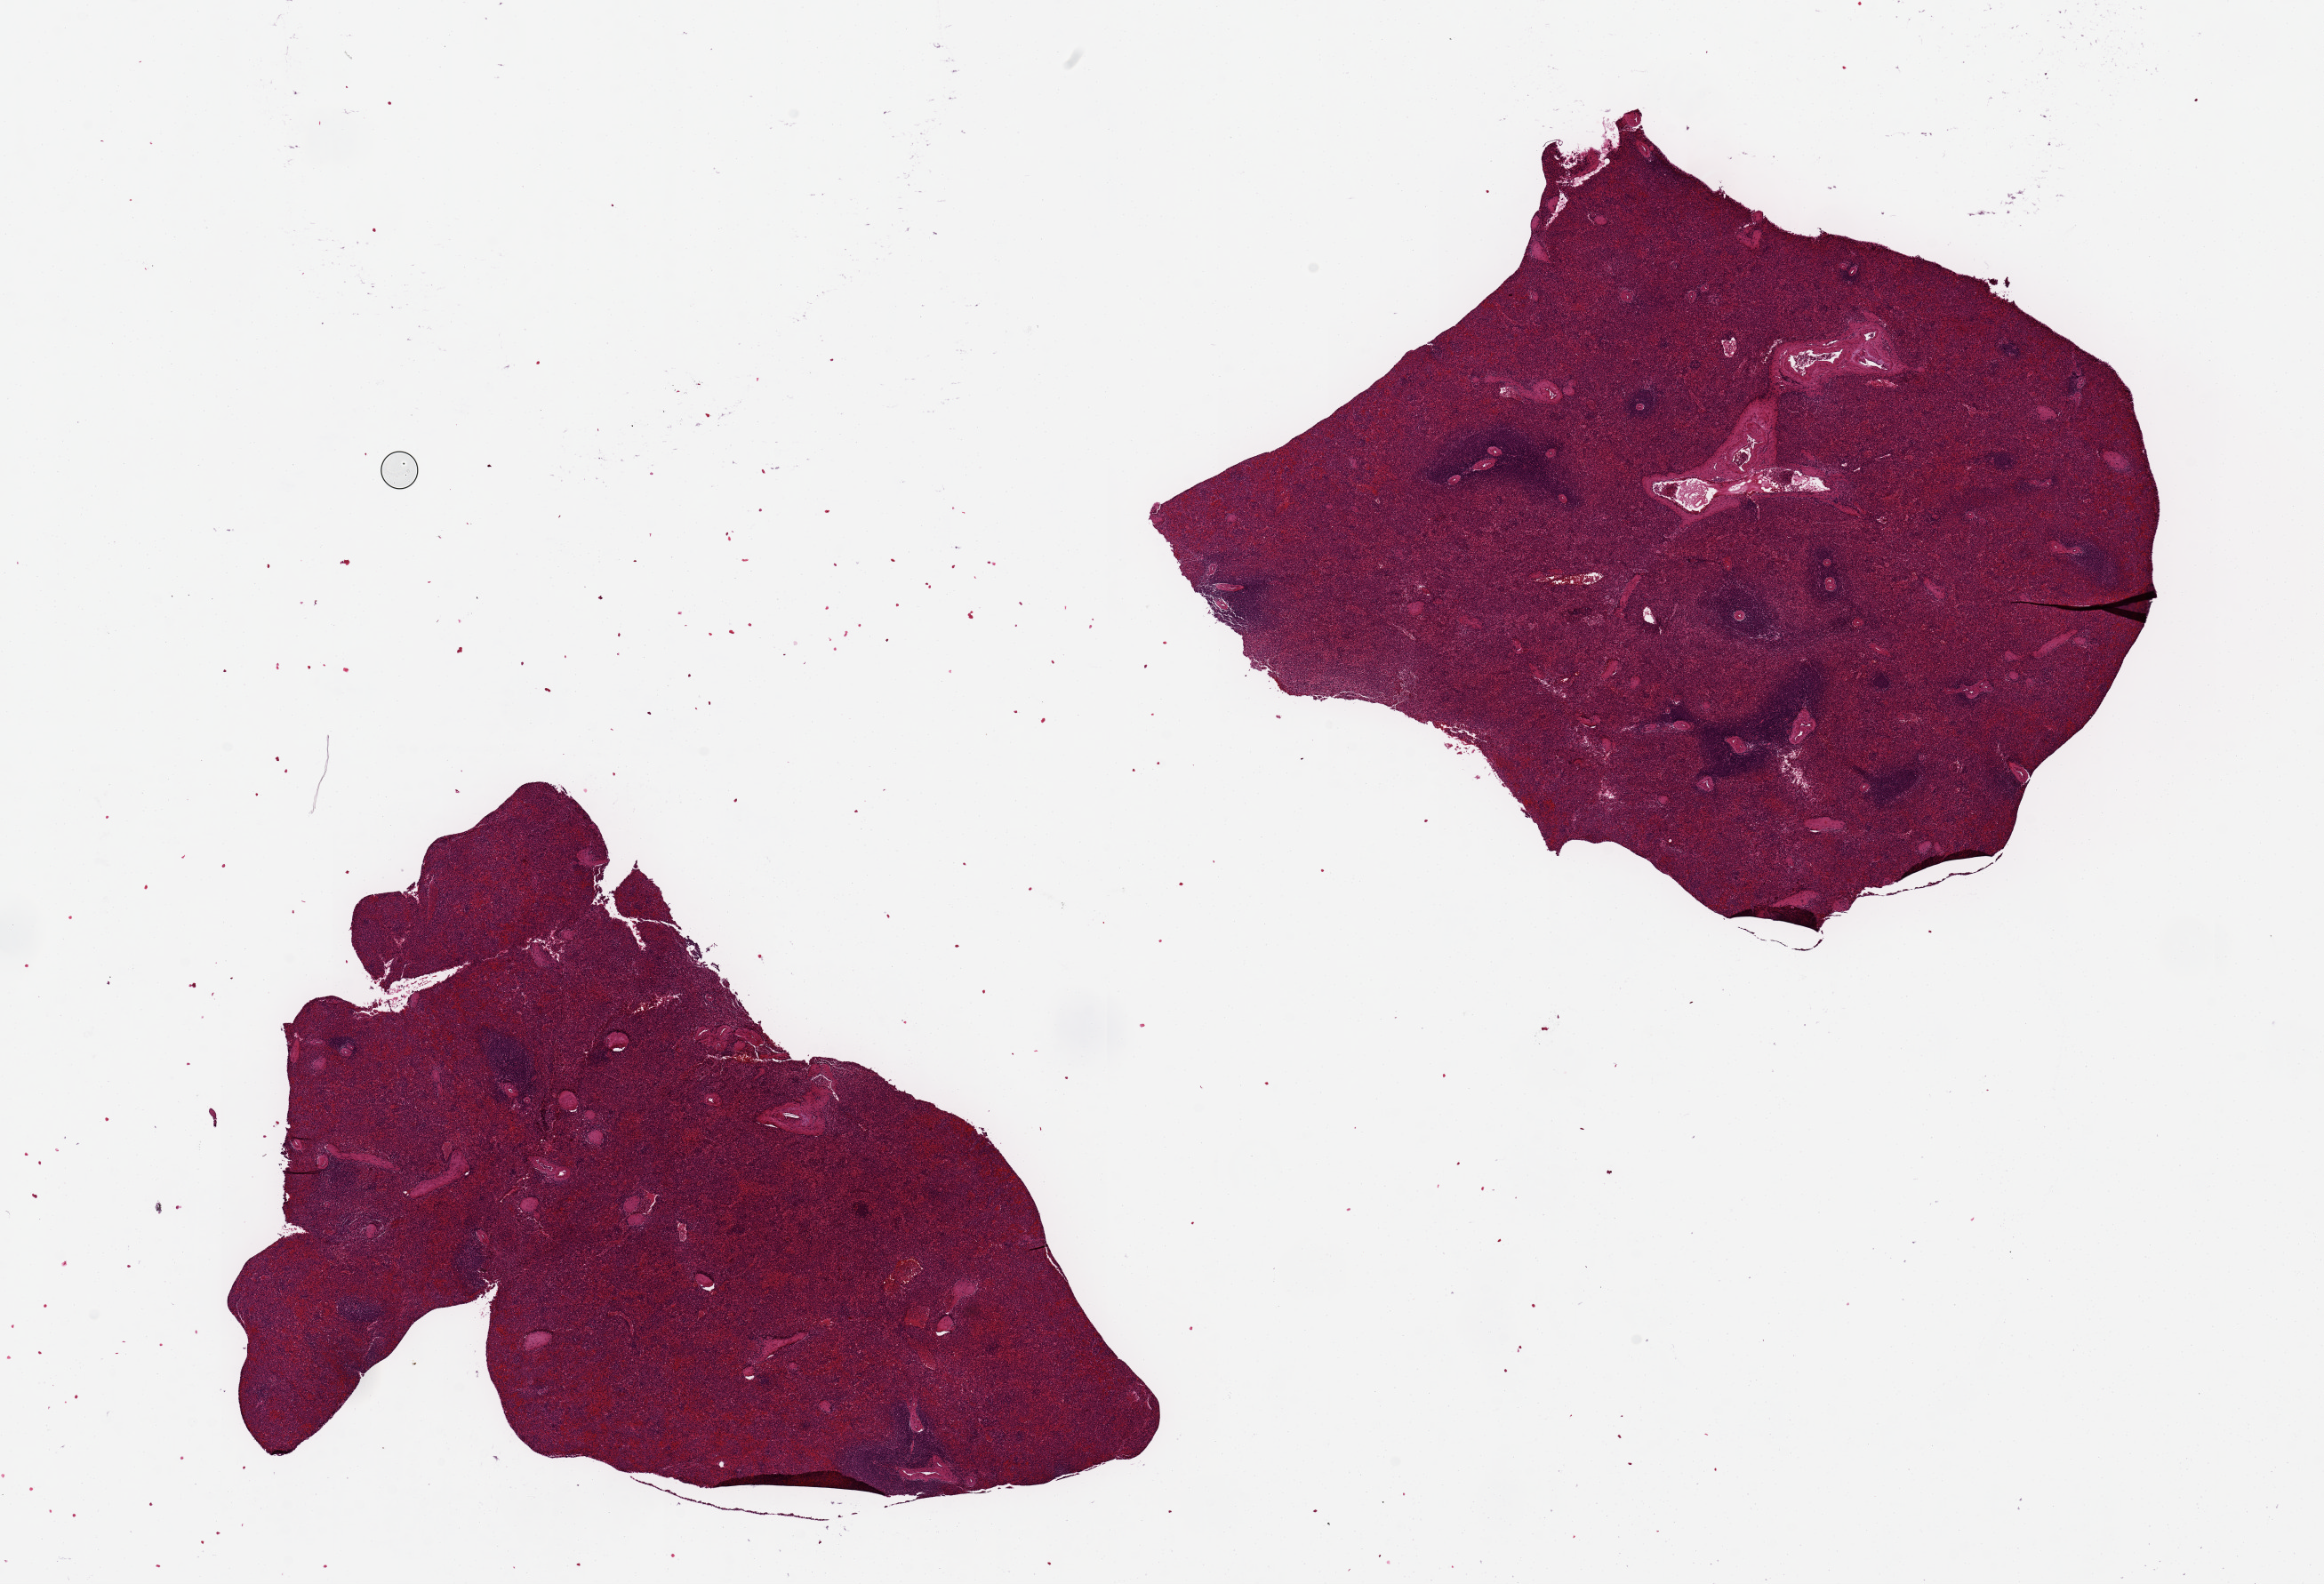
Whole-slide image, H&E stain, low-resolution overview of the scanned area, about 20.7 x 14.1 mm. PAXgene-fixed, paraffin-embedded tissue. Section of spleen (target tissue). Donor tissue sample. Male donor.
Pathologist's review note for this sample: 2 pieces 6x6 & 8x6 mm; mild congestion.